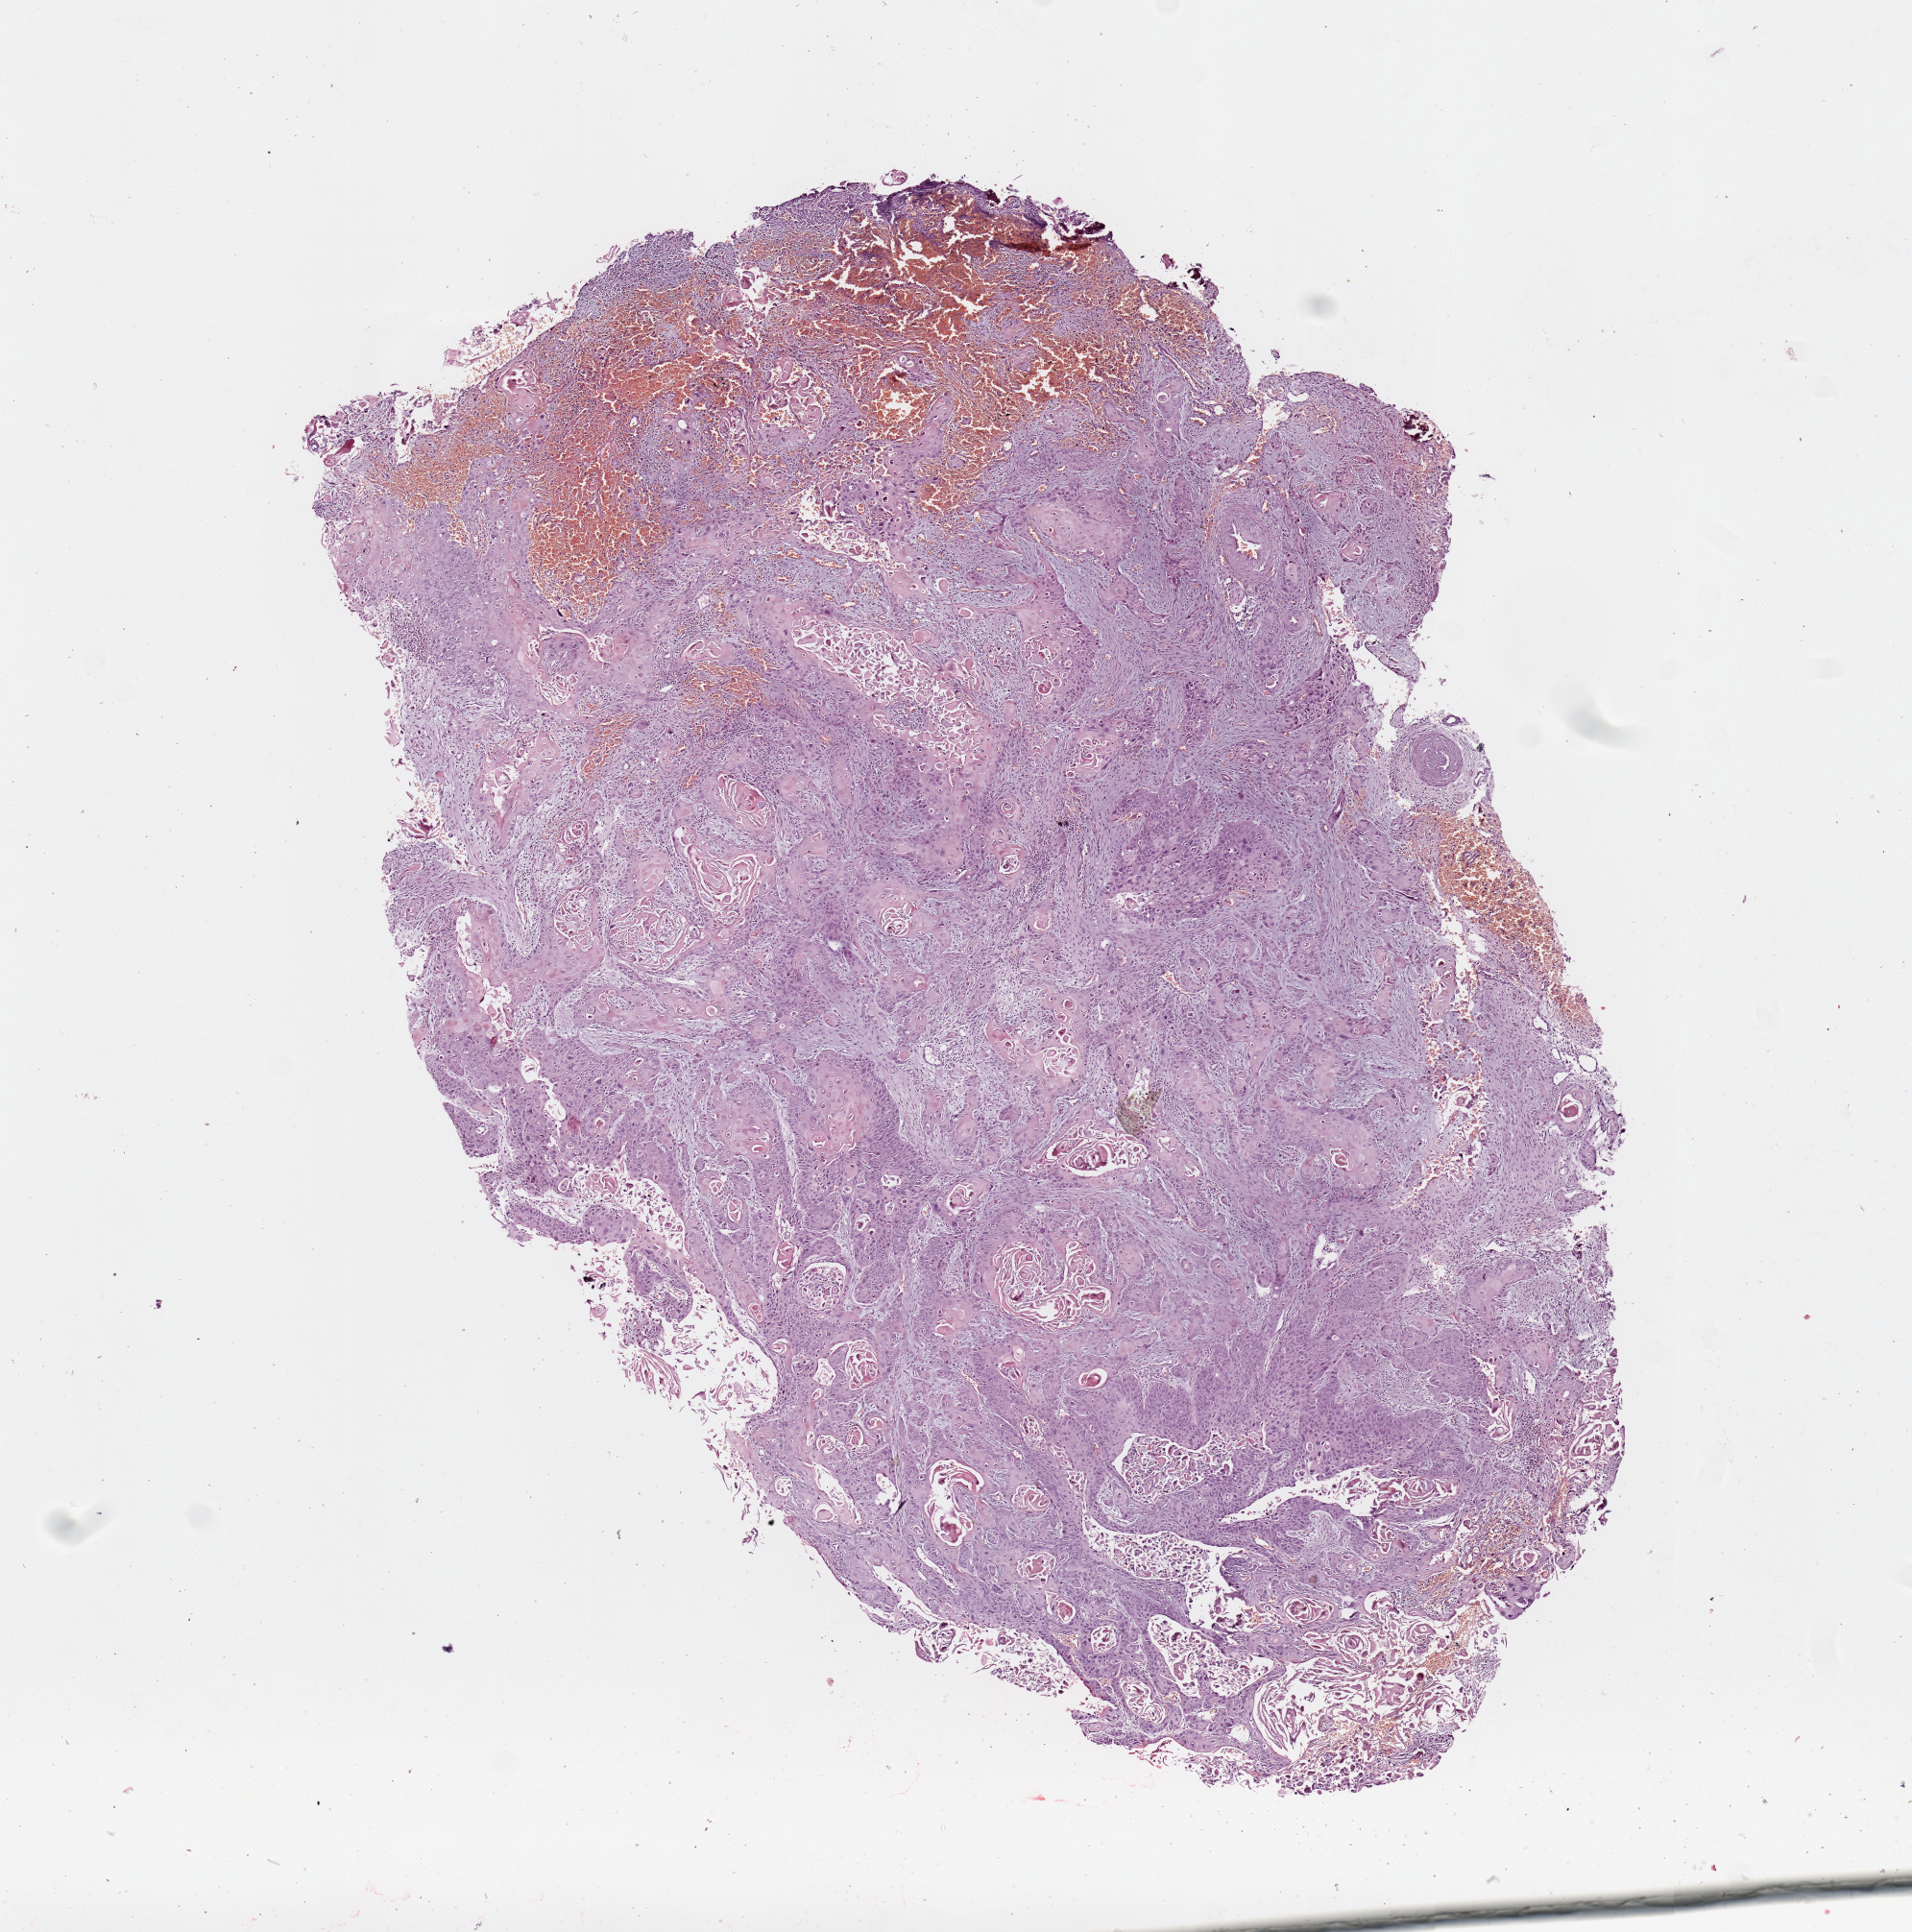
Whole-slide histology image, H&E — a low-resolution overview of the entire scanned area, about 7.9 x 8.0 mm (from a 20x scan). Tumour tissue sample, sampled site: floor of mouth. 58-year-old male patient. Histologic grade: G2 (moderately differentiated). Slide review estimates, as recorded: tumour nuclei 85%, necrosis 3%.
Primary tumour site (as recorded): oral cavity. AJCC pathologic stage: IVA. Diagnosis: Squamous cell carcinoma, NOS.